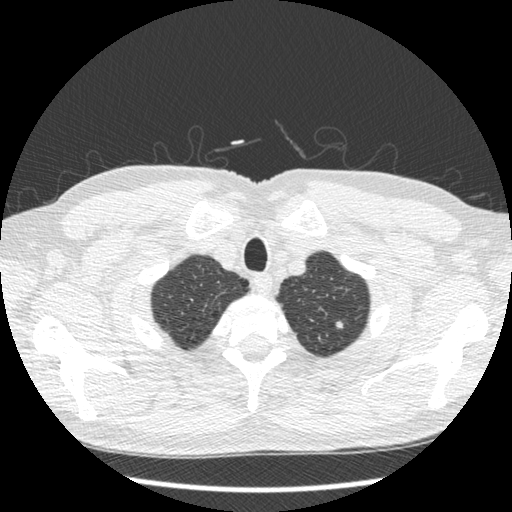
Low-dose screening chest CT, one axial slice. Position 407 of 439 along the scan axis. Lung window (W 1500 / L -600 HU). 1.25 mm slice thickness. 512 × 512 image matrix, field of view 340 × 340 mm.
Annotated regions visible in this slice (expert manual segmentation):
- lesion 1 (nodule, upper lobe of left lung): bounding box <336,322,344,329> (left, top, right, bottom; pixels)